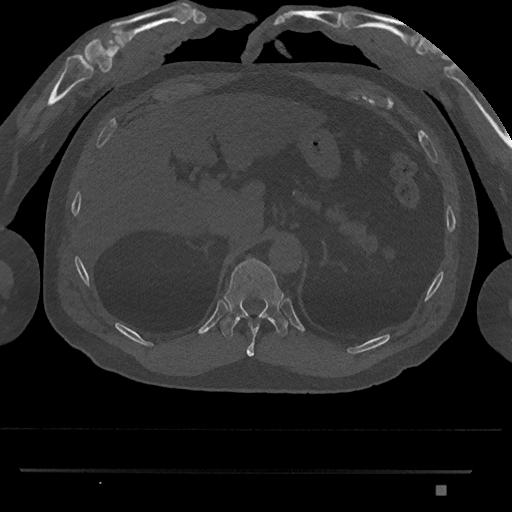
CT including the spine, one axial slice. Slice 962 of 1134 in the series (ordered by position). 120 kVp. Bone window (W 1800 / L 400 HU). 512 × 512 image matrix, field of view 429 × 429 mm. Male patient, age 65 years. Case-level facts recorded for this patient, not image findings: primary cancer: prostate.
Outlined on this slice (semi-automatic segmentation, software-assisted and operator-edited):
- T10 vertebra: bounding box [x1, y1, x2, y2] px = [246, 322, 260, 357]
- T11 vertebra: [220, 258, 288, 340]